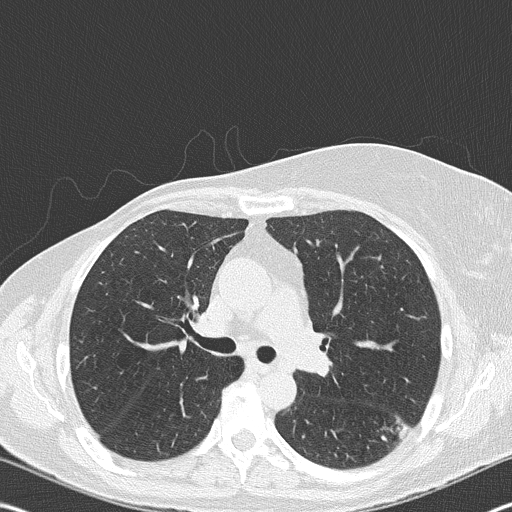
Low-dose screening chest CT, one axial slice; position 114 of 177 along the scan axis; 120 kVp; lung window (W 1500 / L -600 HU); 2 mm slice thickness; 512 × 512 image matrix, field of view 342 × 342 mm.
Annotated regions visible in this slice (manually delineated by an expert):
- lesion 1 (tumor): box from (x=397, y=422) to (x=409, y=438) px